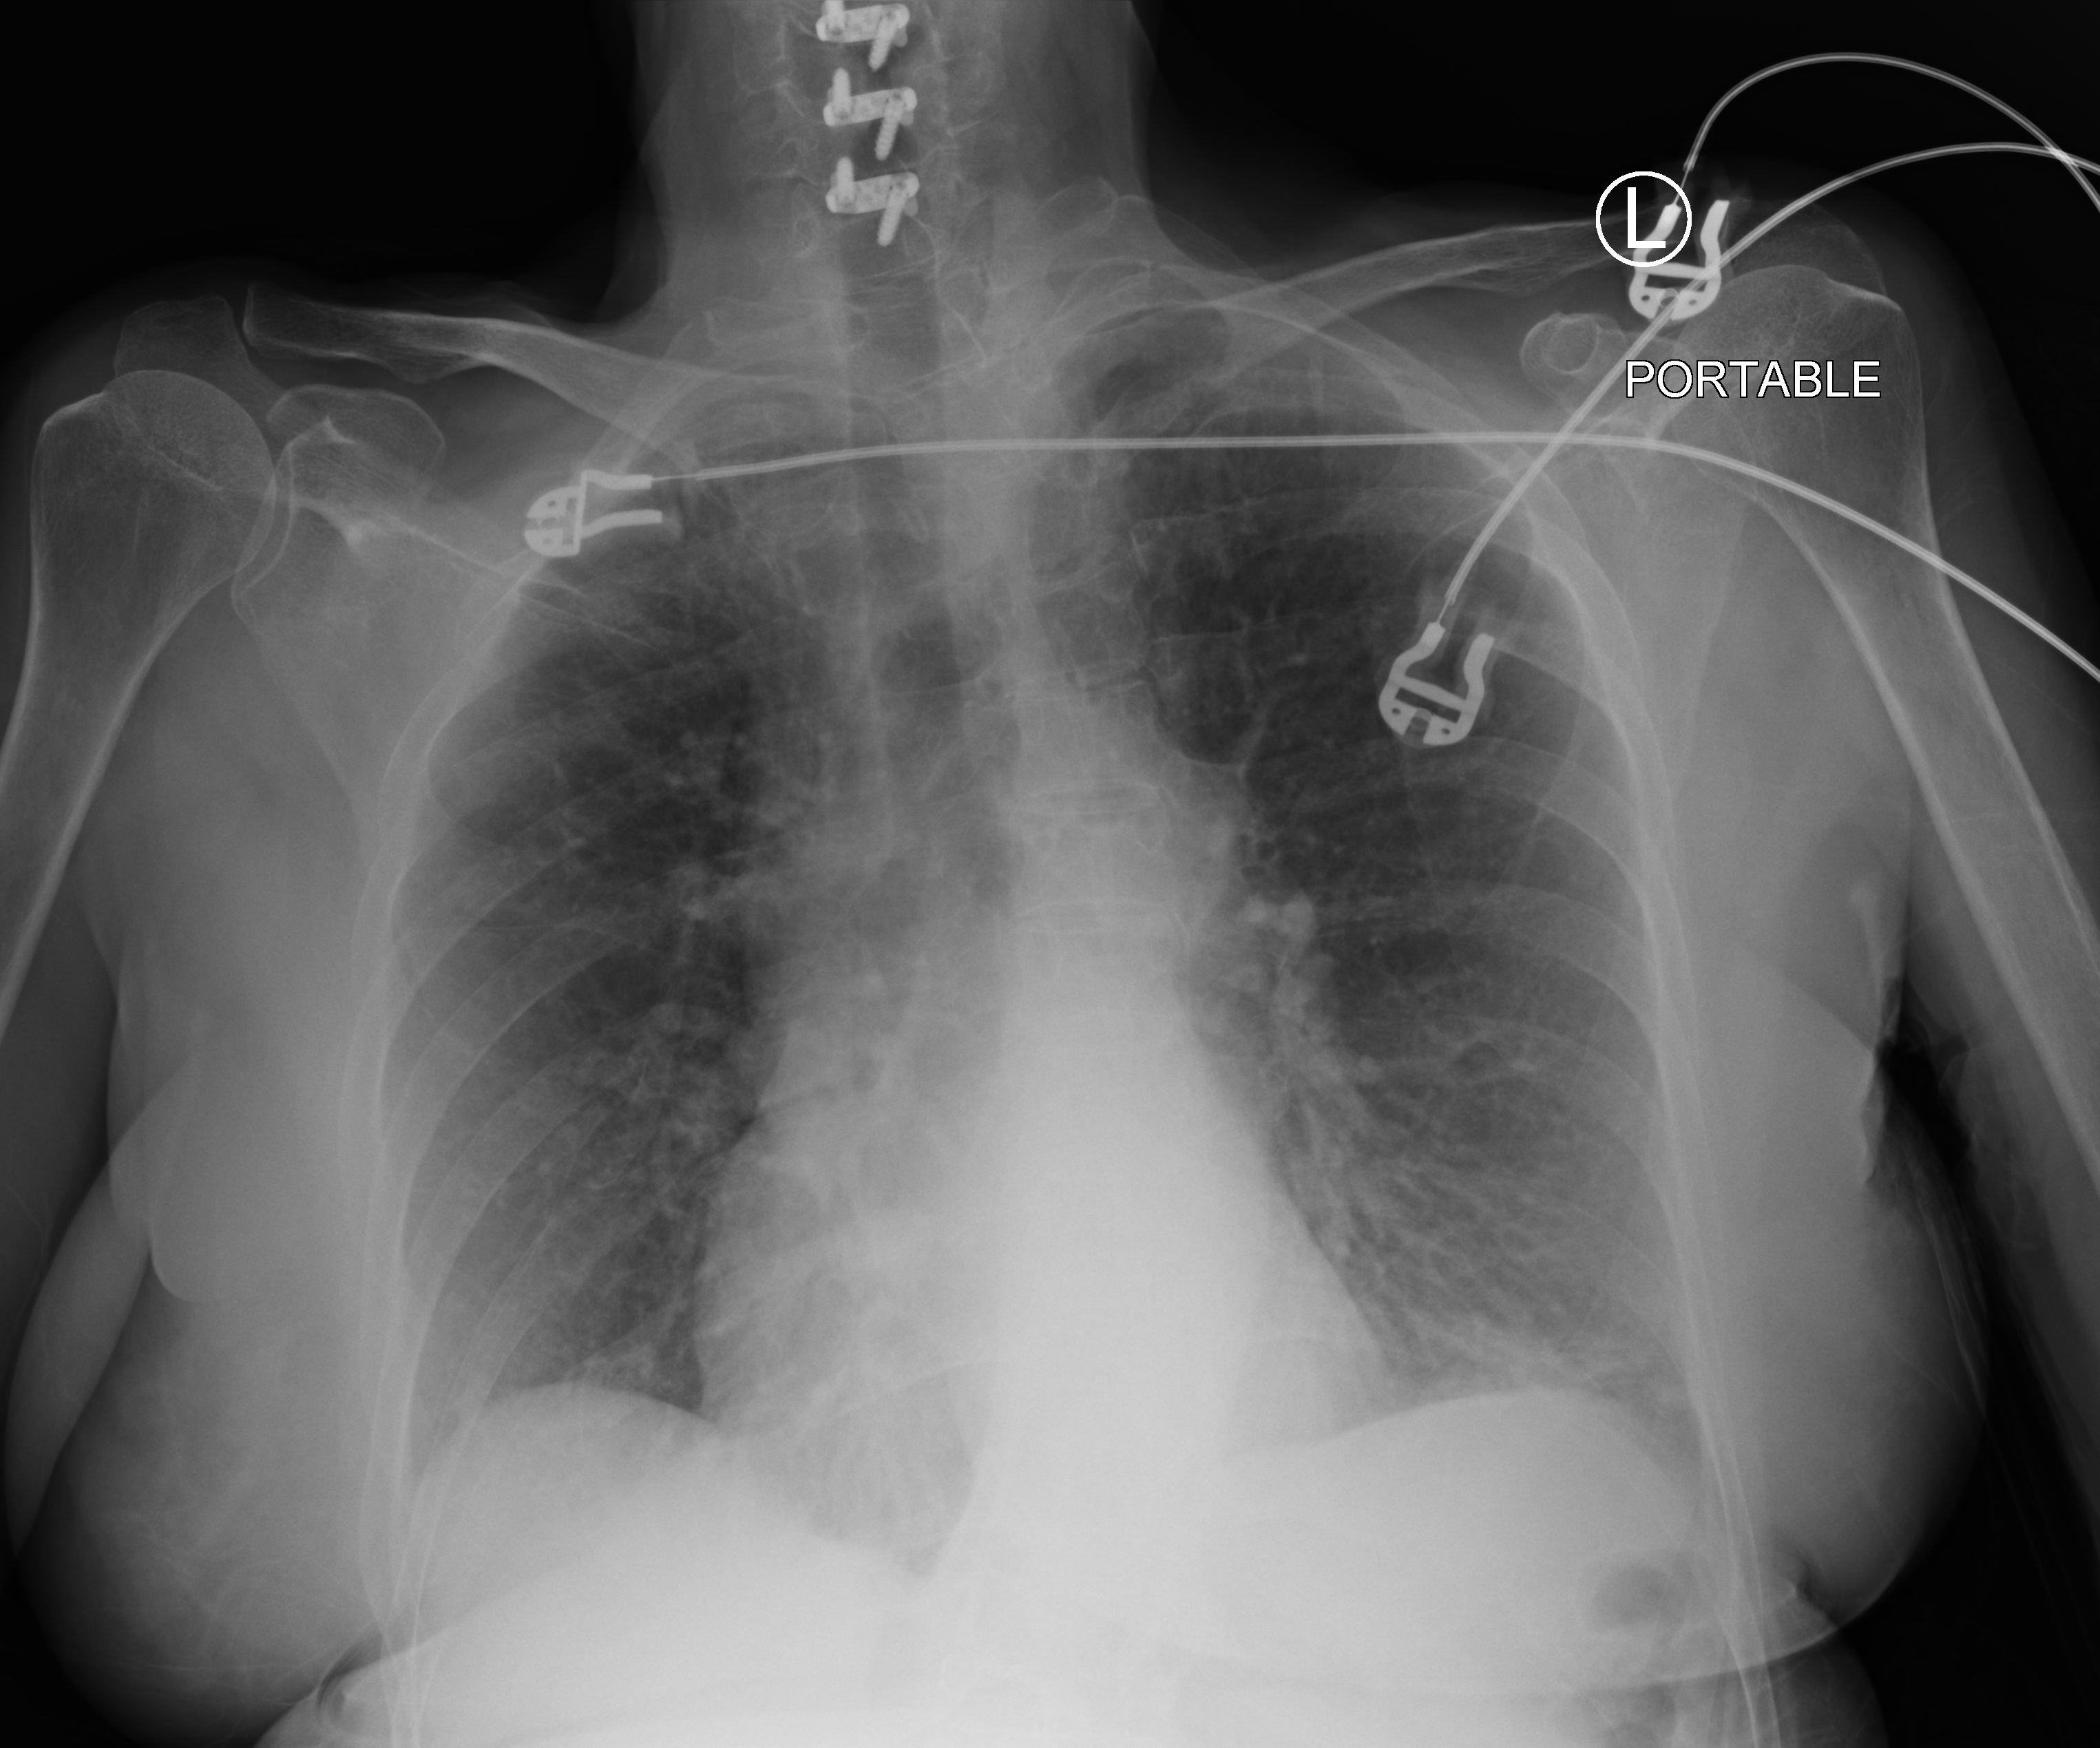
Chest X-ray (portable); anteroposterior (AP) projection. Patient hospitalised with COVID-19; female, aged 60–74 years.
Hospital-stay facts (about this admission, not read from this image; timing relative to this image not recorded): mechanically ventilated during this hospital stay: no.